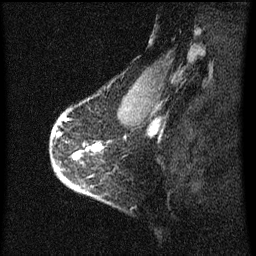
Breast MRI (dynamic contrast-enhanced), one sagittal slice. Slice 49 of 60 in the series (ordered by position). Dynamic contrast-enhanced series, image 2 of 3 at this slice position (ordered by acquisition). 1.5 T. TE 4.2 ms, TR 8 ms. 256 × 256 image matrix, field of view 180 × 180 mm. Female patient, age 56 years.
Structures marked on this image (semi-automatically segmented with operator editing):
- analysis volume of interest (the breast-tissue region the enhancement analysis was run in; not a lesion): bounding box [x1, y1, x2, y2] px = [54, 110, 103, 193]
- tumour enhancement mask (voxels above the 70 % enhancement threshold inside the analysis volume of interest): [96, 146, 103, 151]